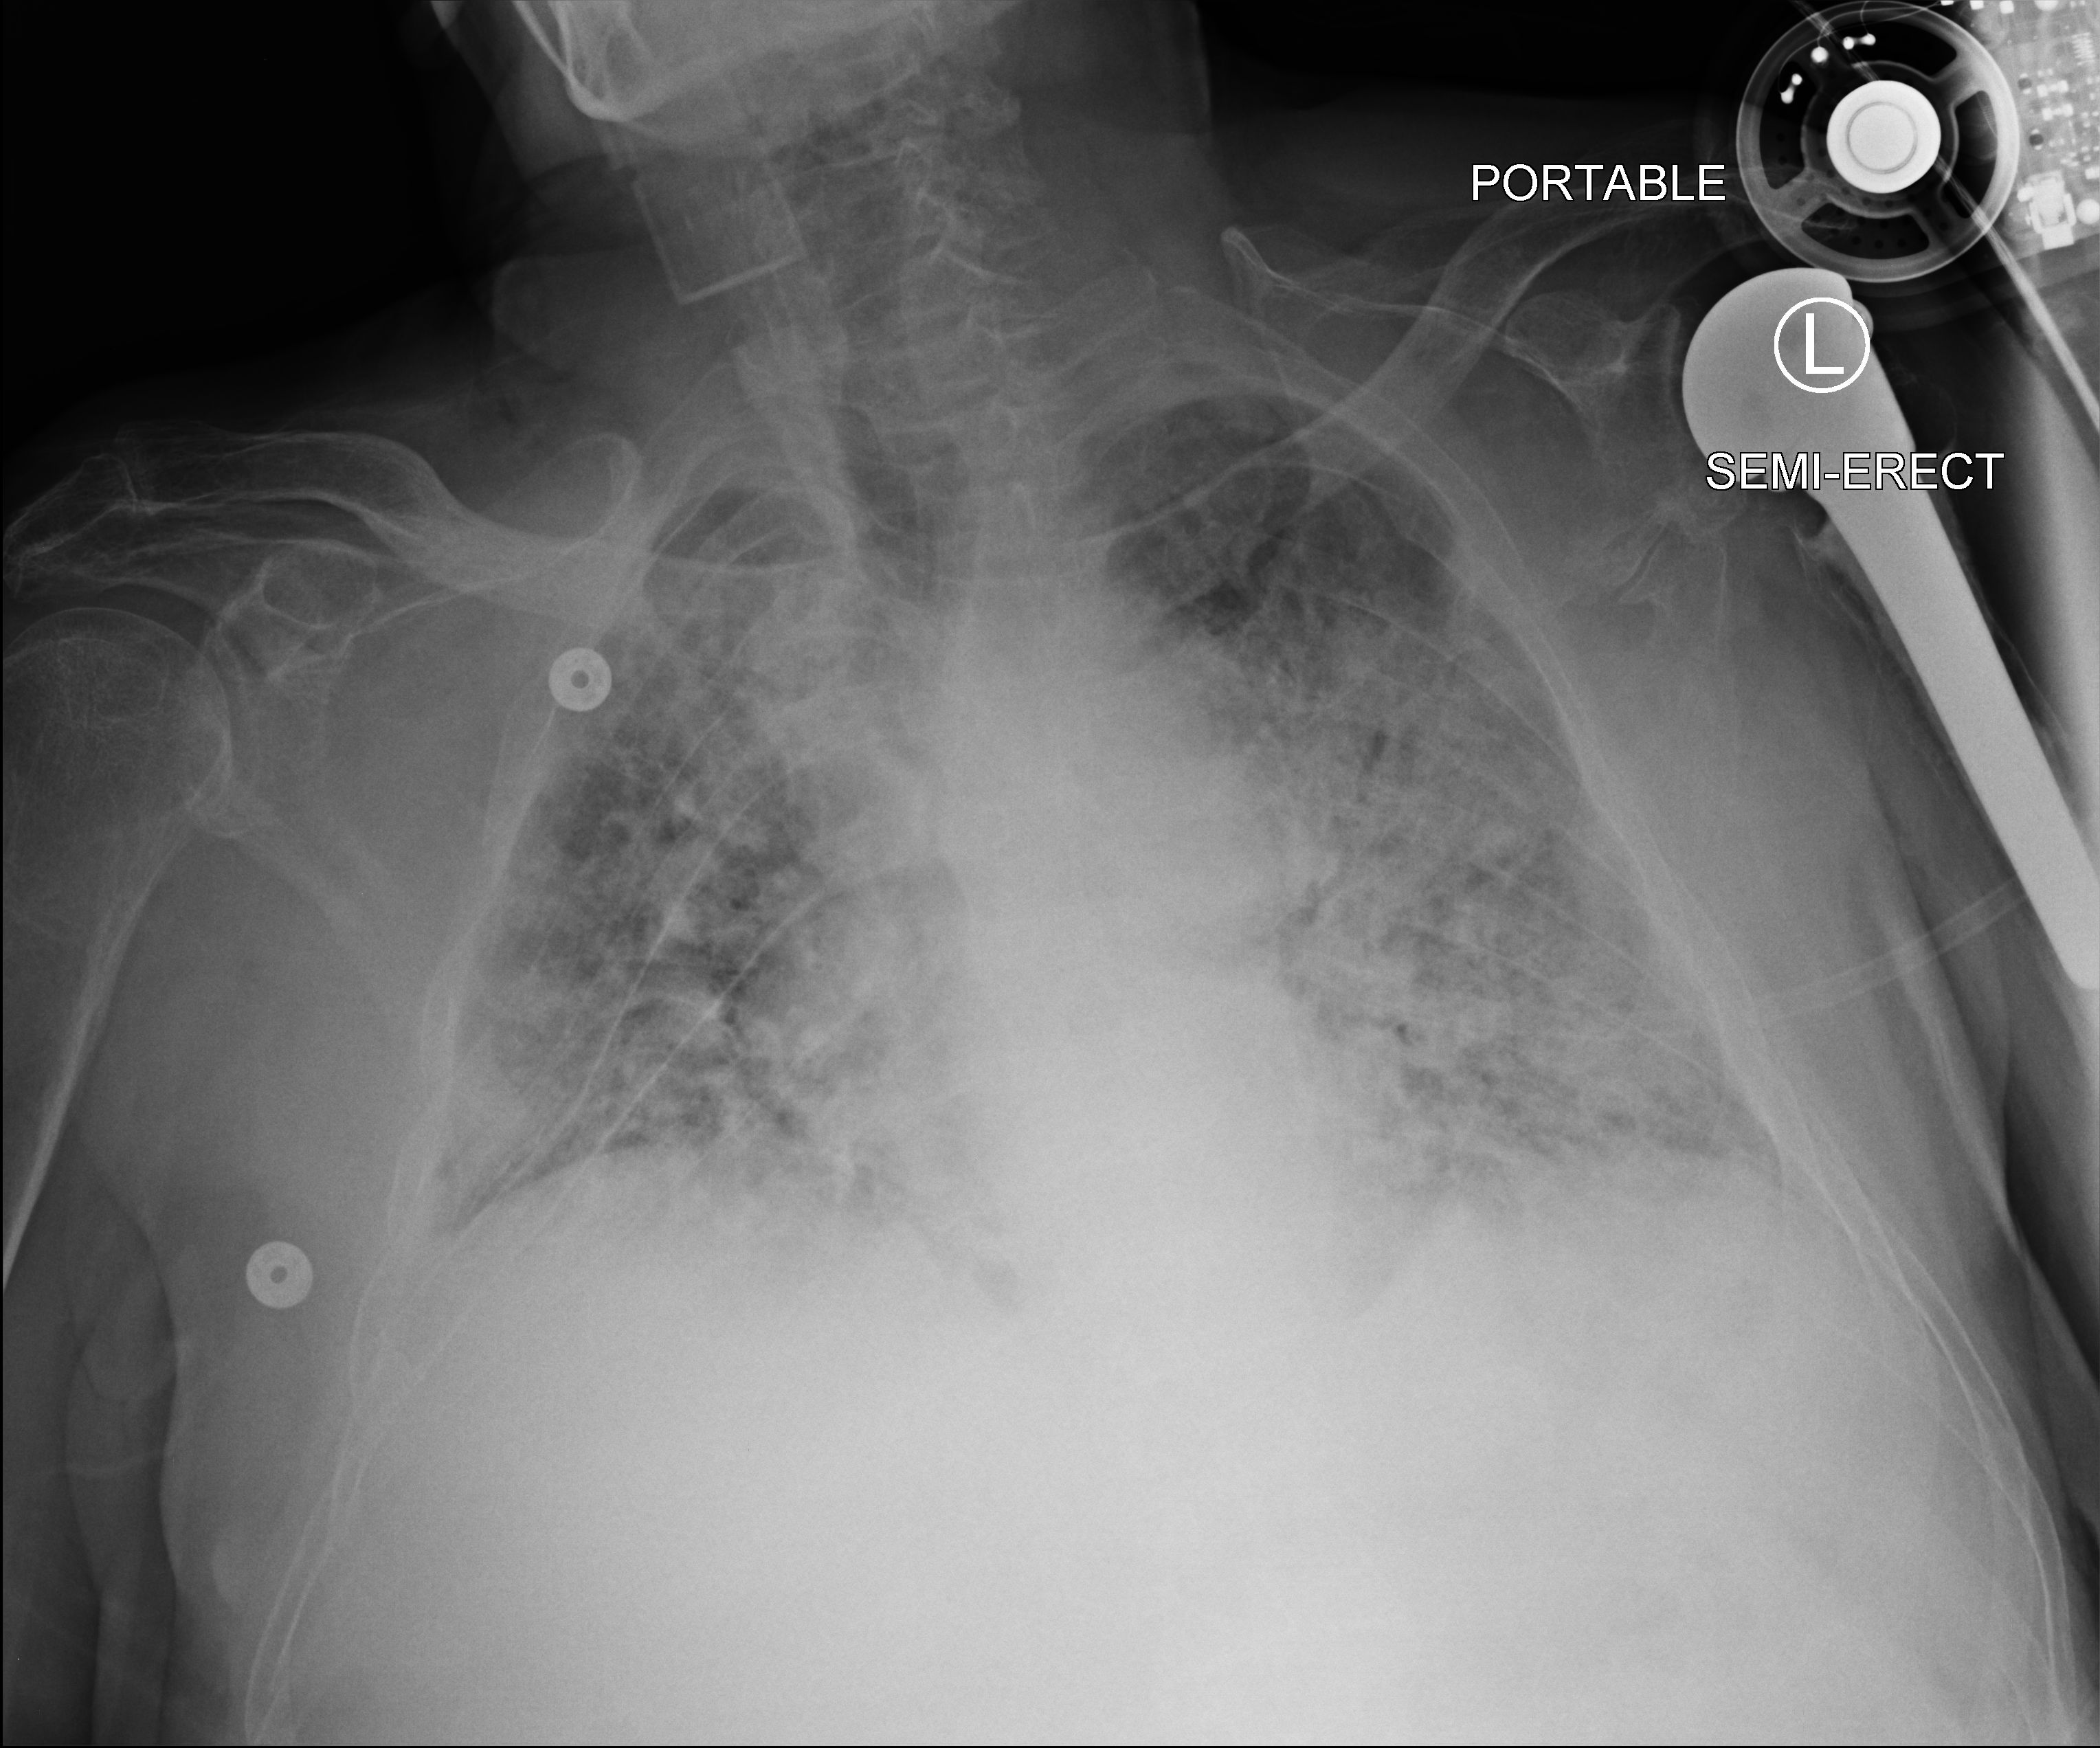
Chest X-ray (portable); anteroposterior (AP) projection. Male patient hospitalised with COVID-19, age 60–74 years.
Admission-level facts for this patient (not findings on this image; timing relative to this image not recorded): mechanically ventilated during this hospital stay: no; admitted to intensive care during this hospital stay: no; diabetes (admission record): no.